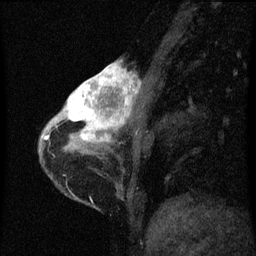
Breast MRI (dynamic contrast-enhanced), one sagittal slice; slice 16 of 60 in the series (ordered by position); dynamic contrast-enhanced series, image 2 of 3 at this slice position (ordered by acquisition); 1.5 T; TE 4.2 ms, TR 8 ms; 256 × 256 image matrix, field of view 180 × 180 mm. Female patient, age 38 years.
Outlined on this slice (semi-automatic segmentation, software-assisted and operator-edited):
- analysis volume of interest (the breast-tissue region the enhancement analysis was run in; not a lesion): bounding box [x1, y1, x2, y2] px = [61, 62, 146, 147]
- tumour enhancement mask (voxels above the 70 % enhancement threshold inside the analysis volume of interest): [63, 62, 139, 143]